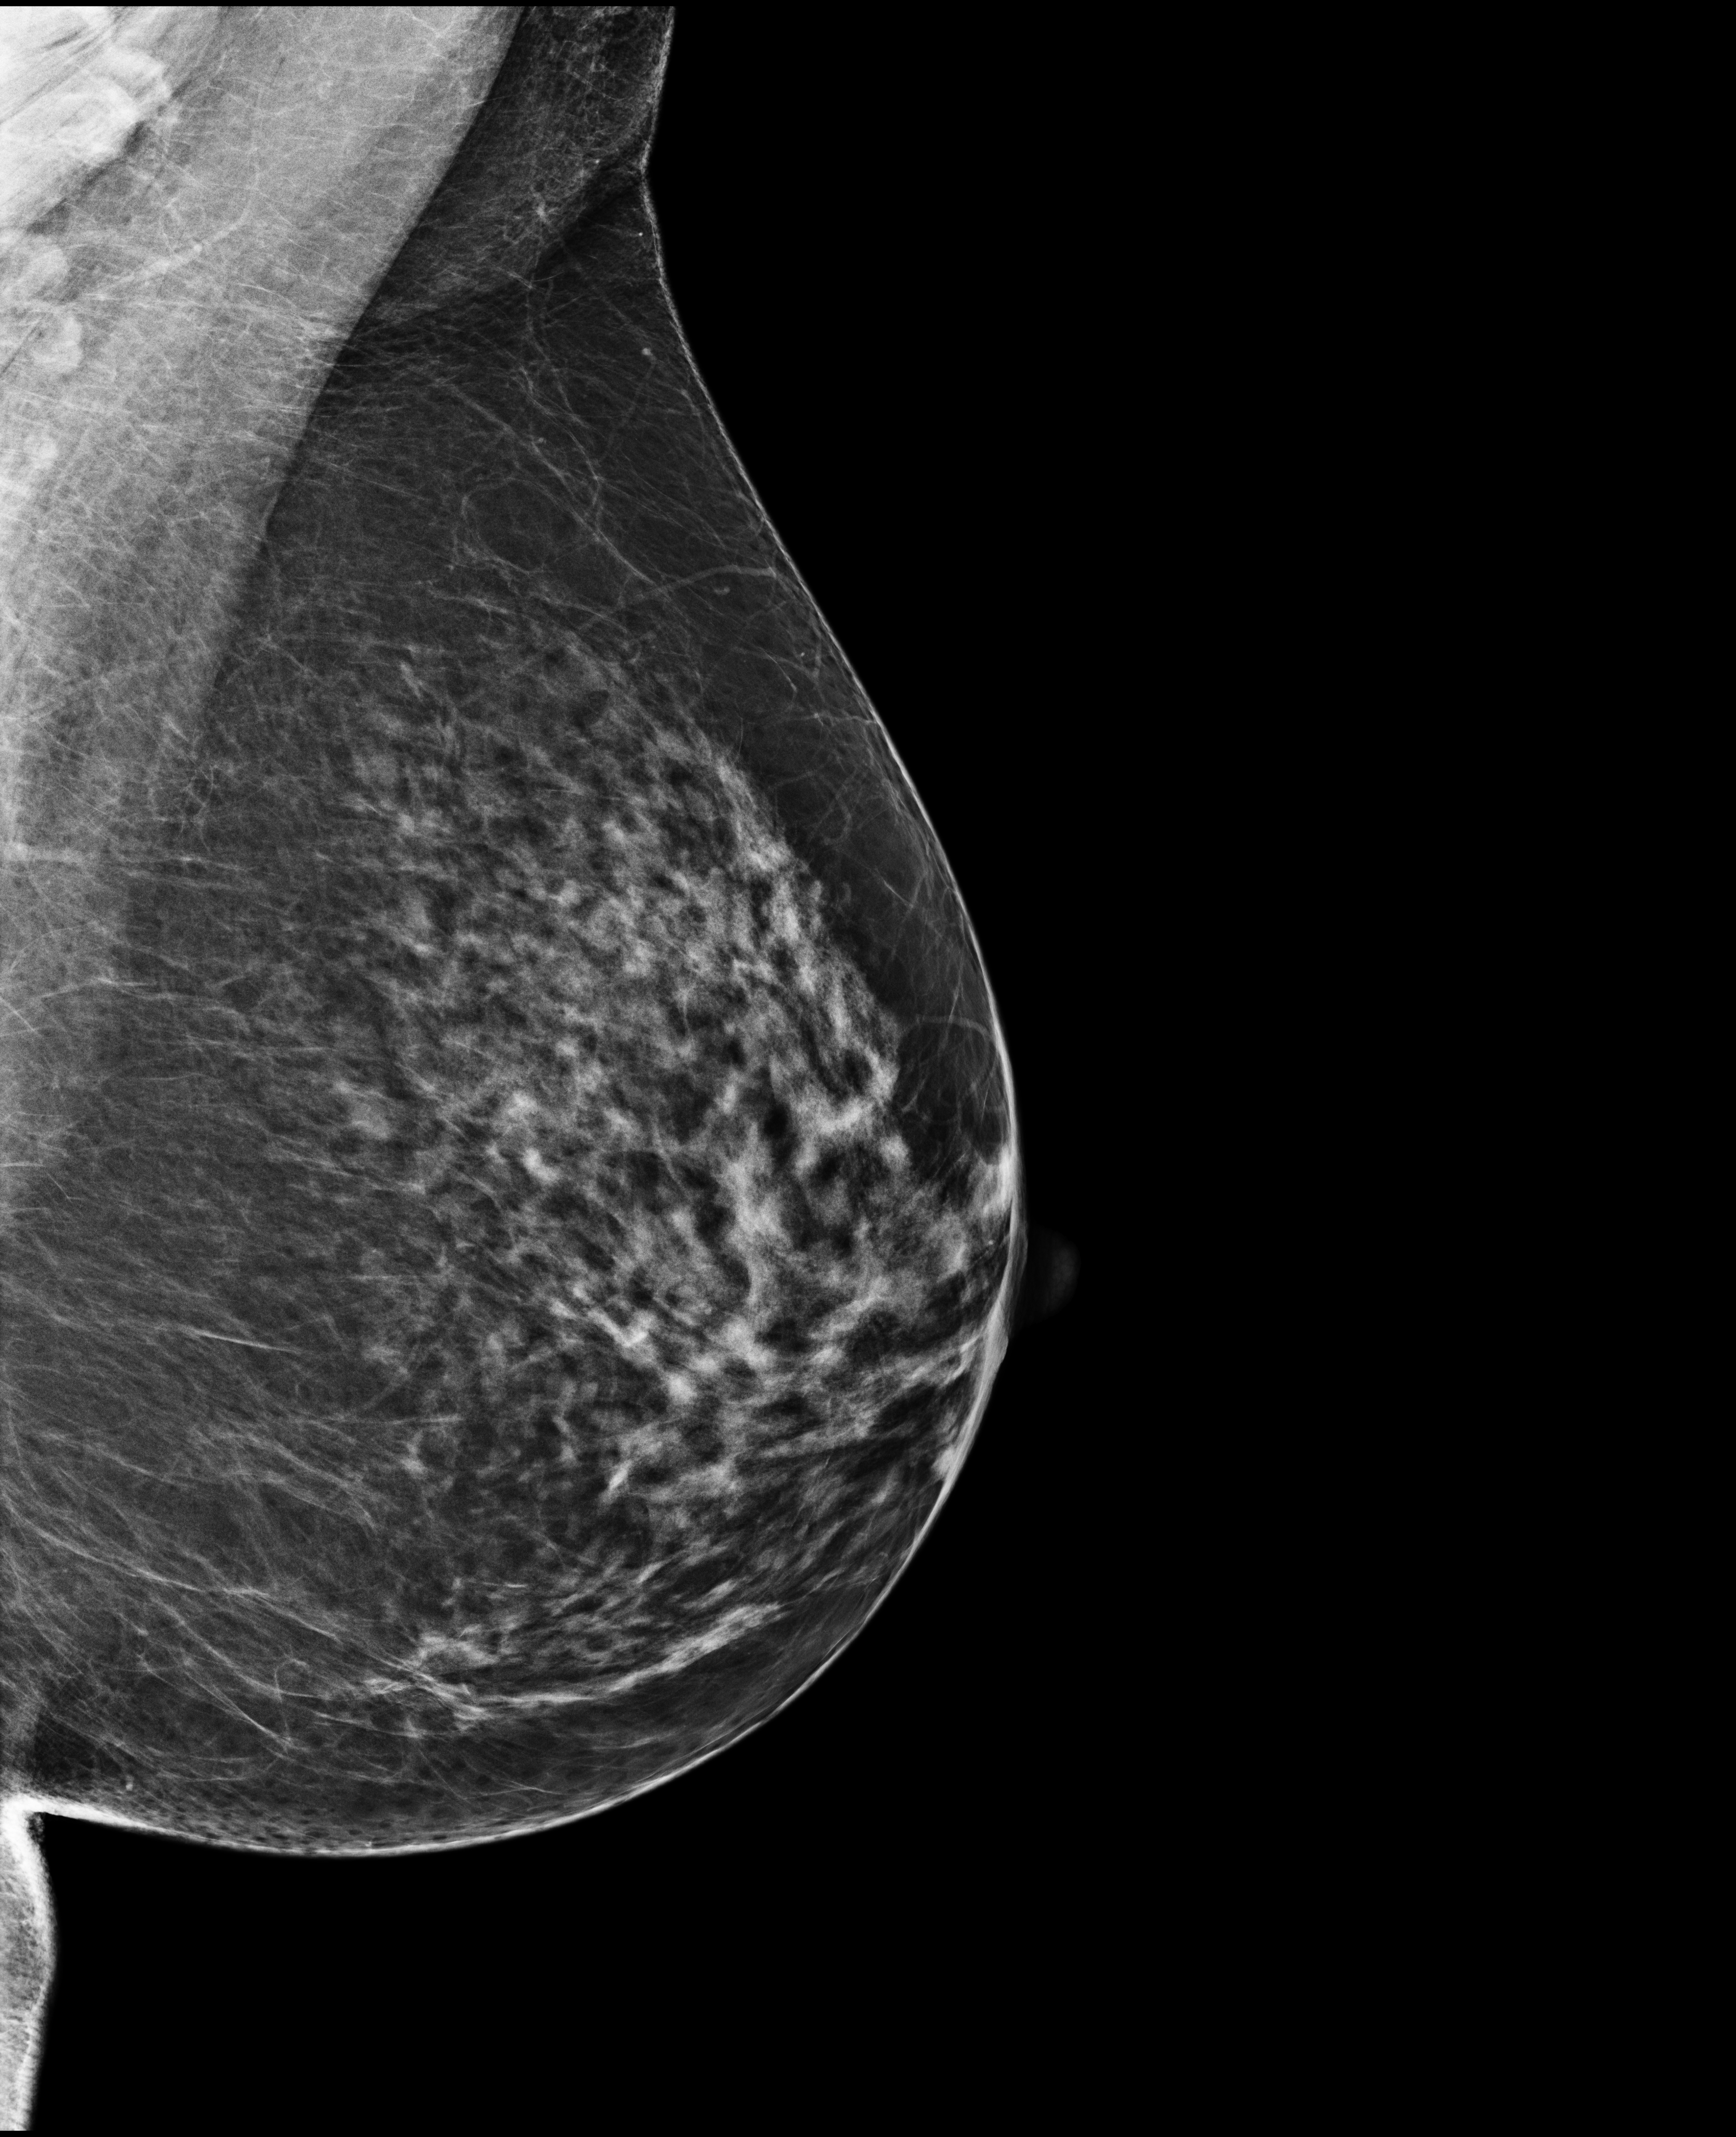
Full-field digital mammogram (FFDM), left breast, medio-lateral oblique projection, annual screening mammography examination. Female patient, age 52 years.
BI-RADS breast density category at the screening exam (both breasts, scale 1–4): 3. Final BI-RADS category for the screening round (tomosynthesis exam, both breasts): category 1. Recall: no recall after this screen.